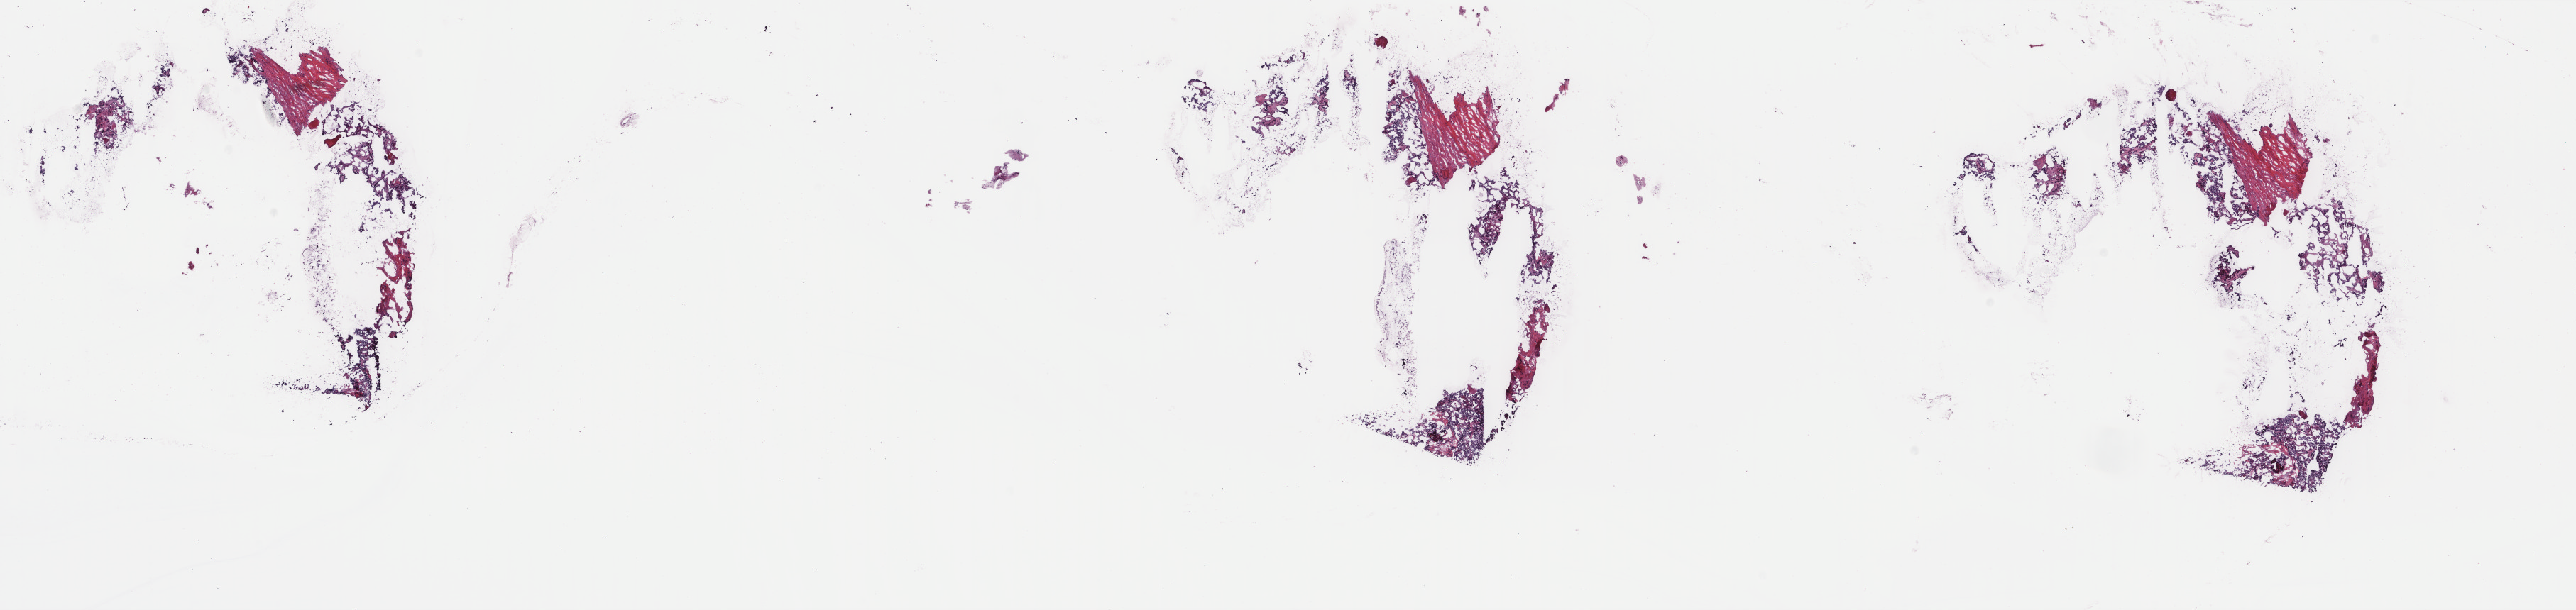
H&E whole-slide image — a low-resolution overview of the entire scanned area, about 28.8 x 6.8 mm; frozen section; sample: primary tumour, thyroid. Male patient; age at initial diagnosis 36 years. Slide review estimates, as recorded: tumour cells 65%, tumour nuclei 90%, normal cells 10%, stromal cells 25%, necrosis 0%. Infiltration values recorded for this section: lymphocyte infiltration 0%, monocyte infiltration 0%, neutrophil infiltration 0%.
• laterality: left
• AJCC pathologic stage: I
• pathologic diagnosis: Papillary adenocarcinoma, NOS (thyroid gland)